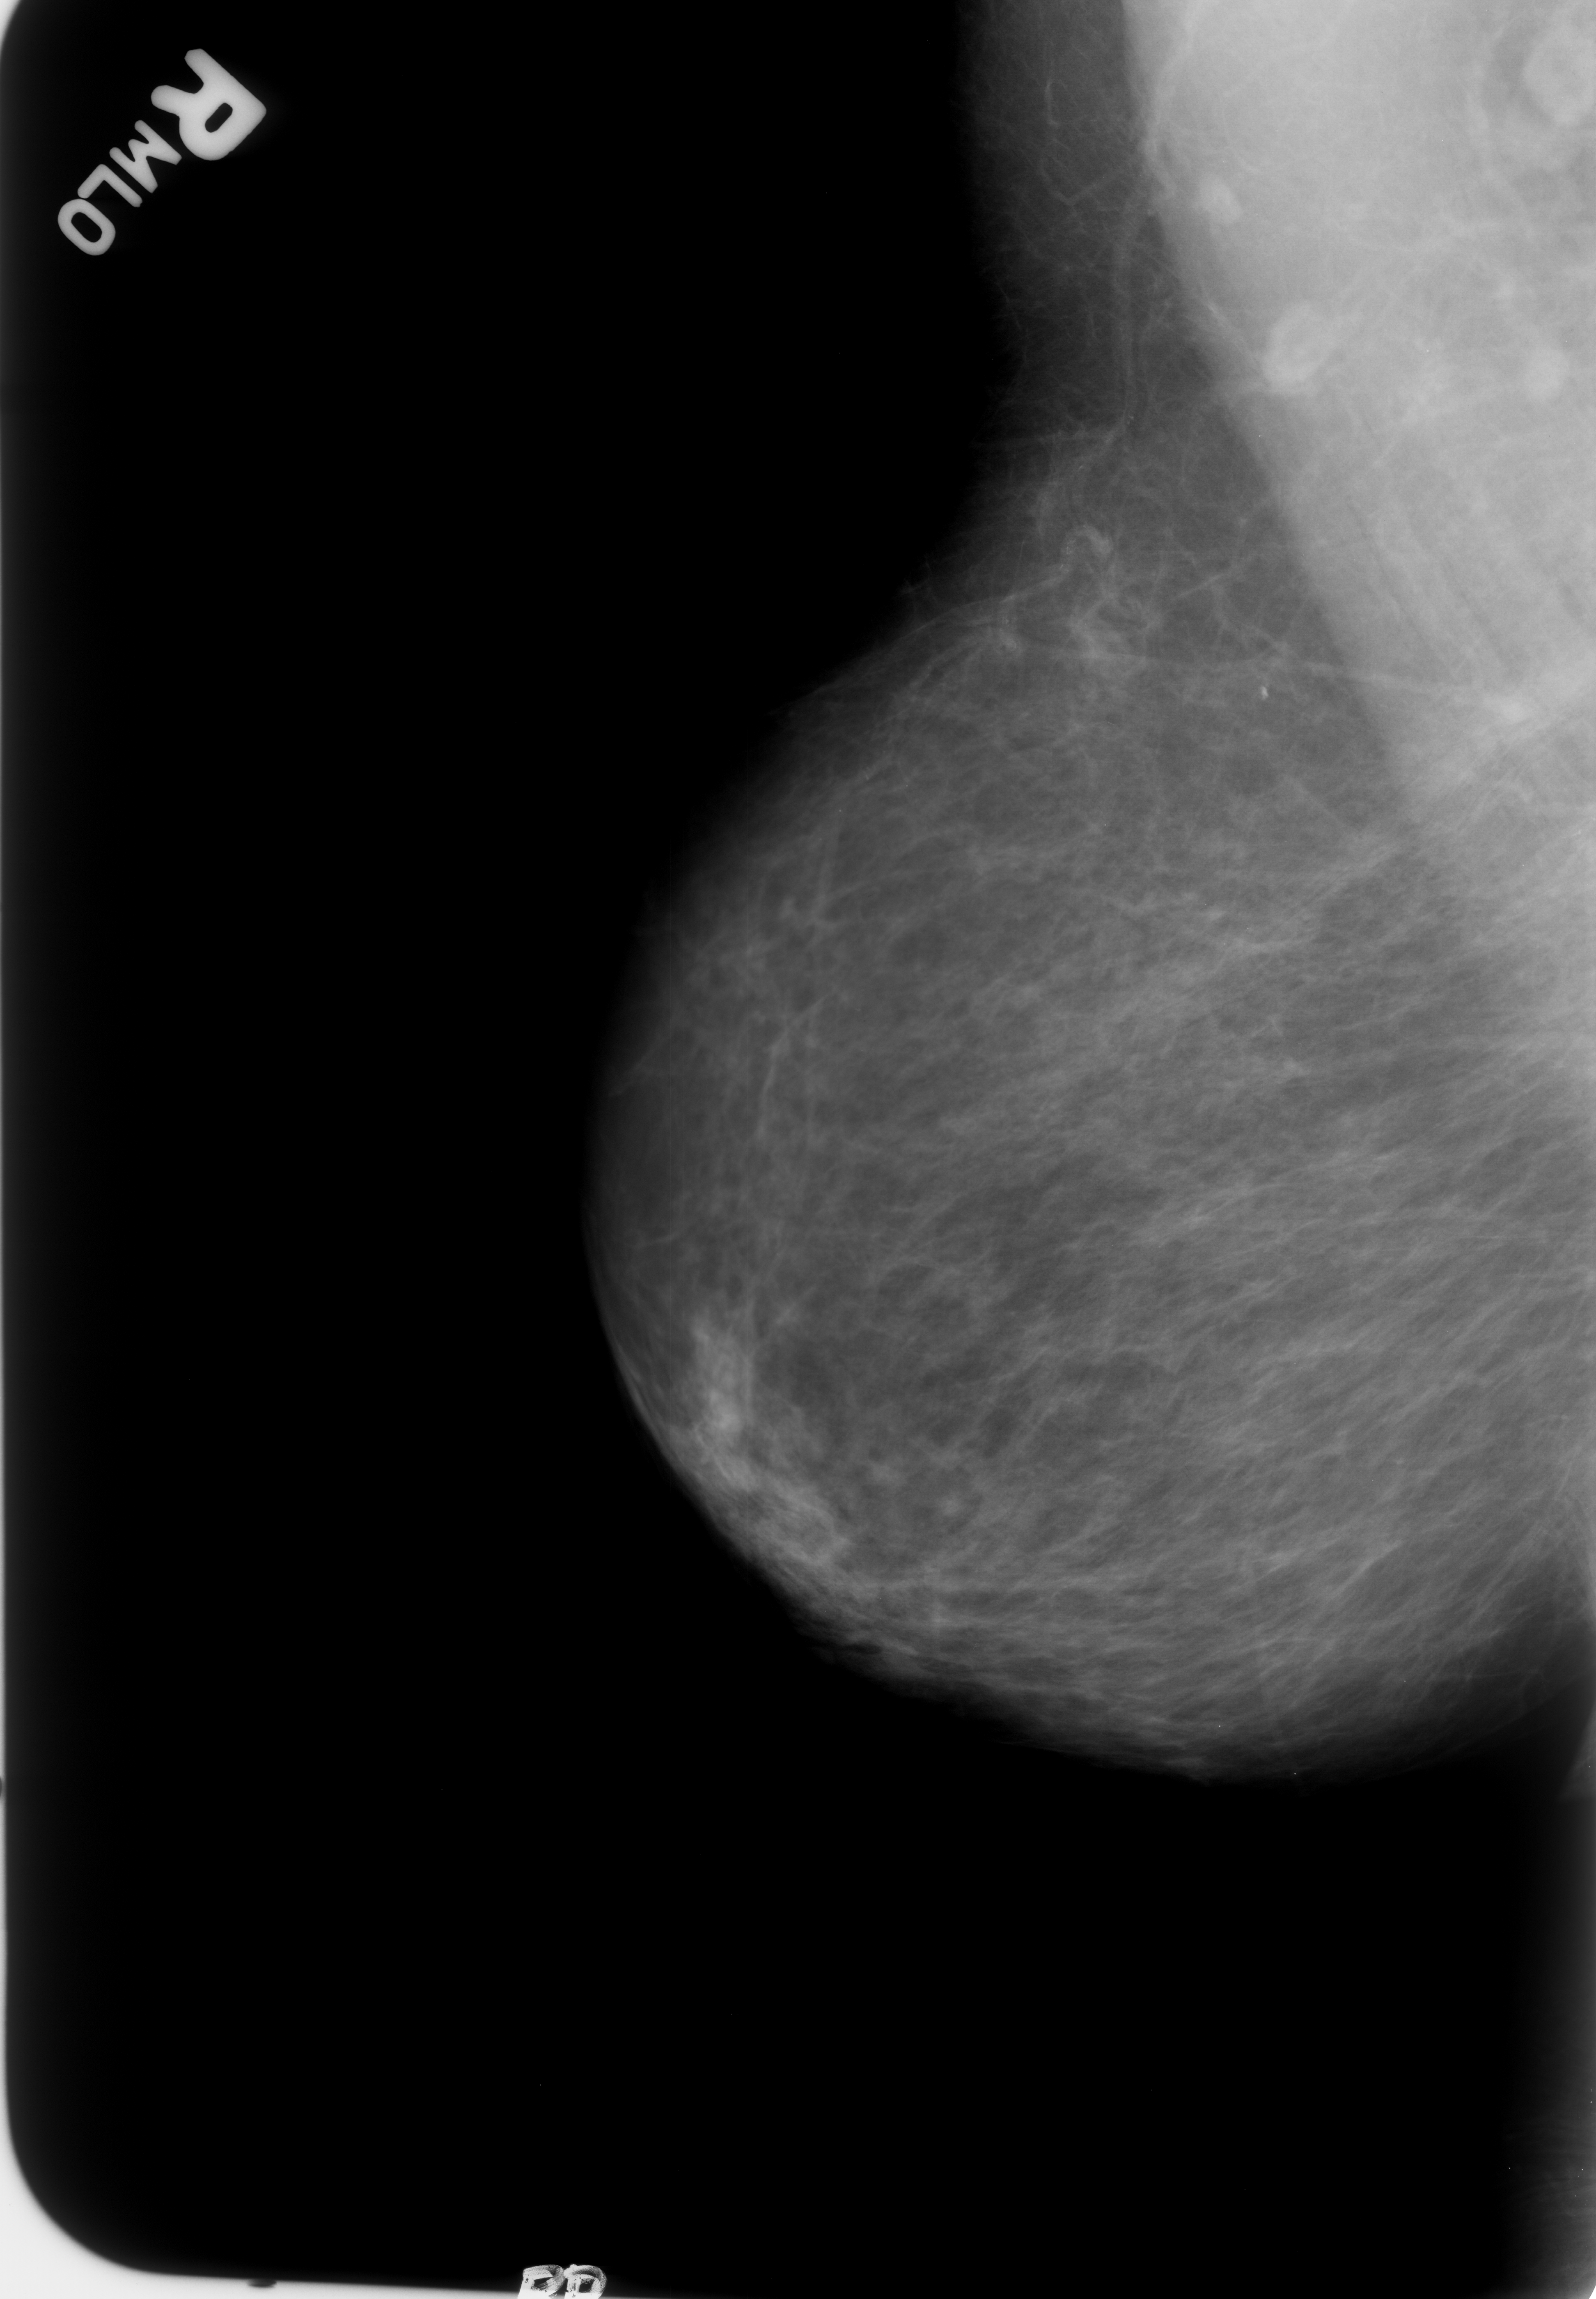
Mammogram (digitized film); right breast; MLO view; BI-RADS breast density category 1 (scale 1–4); 1596 × 2299 image matrix.
Expert-marked regions of interest on this film, with their recorded descriptors:
- Finding 1 of 3: mass, shape oval / lymph node, margins circumscribed; BI-RADS assessment category 2; subtlety rating 4 on a 1 (subtle) to 5 (obvious) scale; outcome (as recorded, no biopsy): benign without callback (not worked up further): bounding box (x1, y1, x2, y2) in pixels: (1173, 168, 1252, 242)
- Finding 2 of 3: mass, shape oval / lymph node, margins circumscribed; BI-RADS assessment category 2; subtlety rating 4 on a 1 (subtle) to 5 (obvious) scale; benign; no additional work-up was recommended (outcome (as recorded, no biopsy): benign without callback): (1244, 302, 1347, 402)
- Finding 3 of 3: mass, shape oval / lymph node, margins circumscribed; BI-RADS assessment category 2; subtlety rating 4 on a 1 (subtle) to 5 (obvious) scale; benign; no additional work-up was recommended (outcome (as recorded, no biopsy): benign without callback): (1504, 325, 1583, 408)